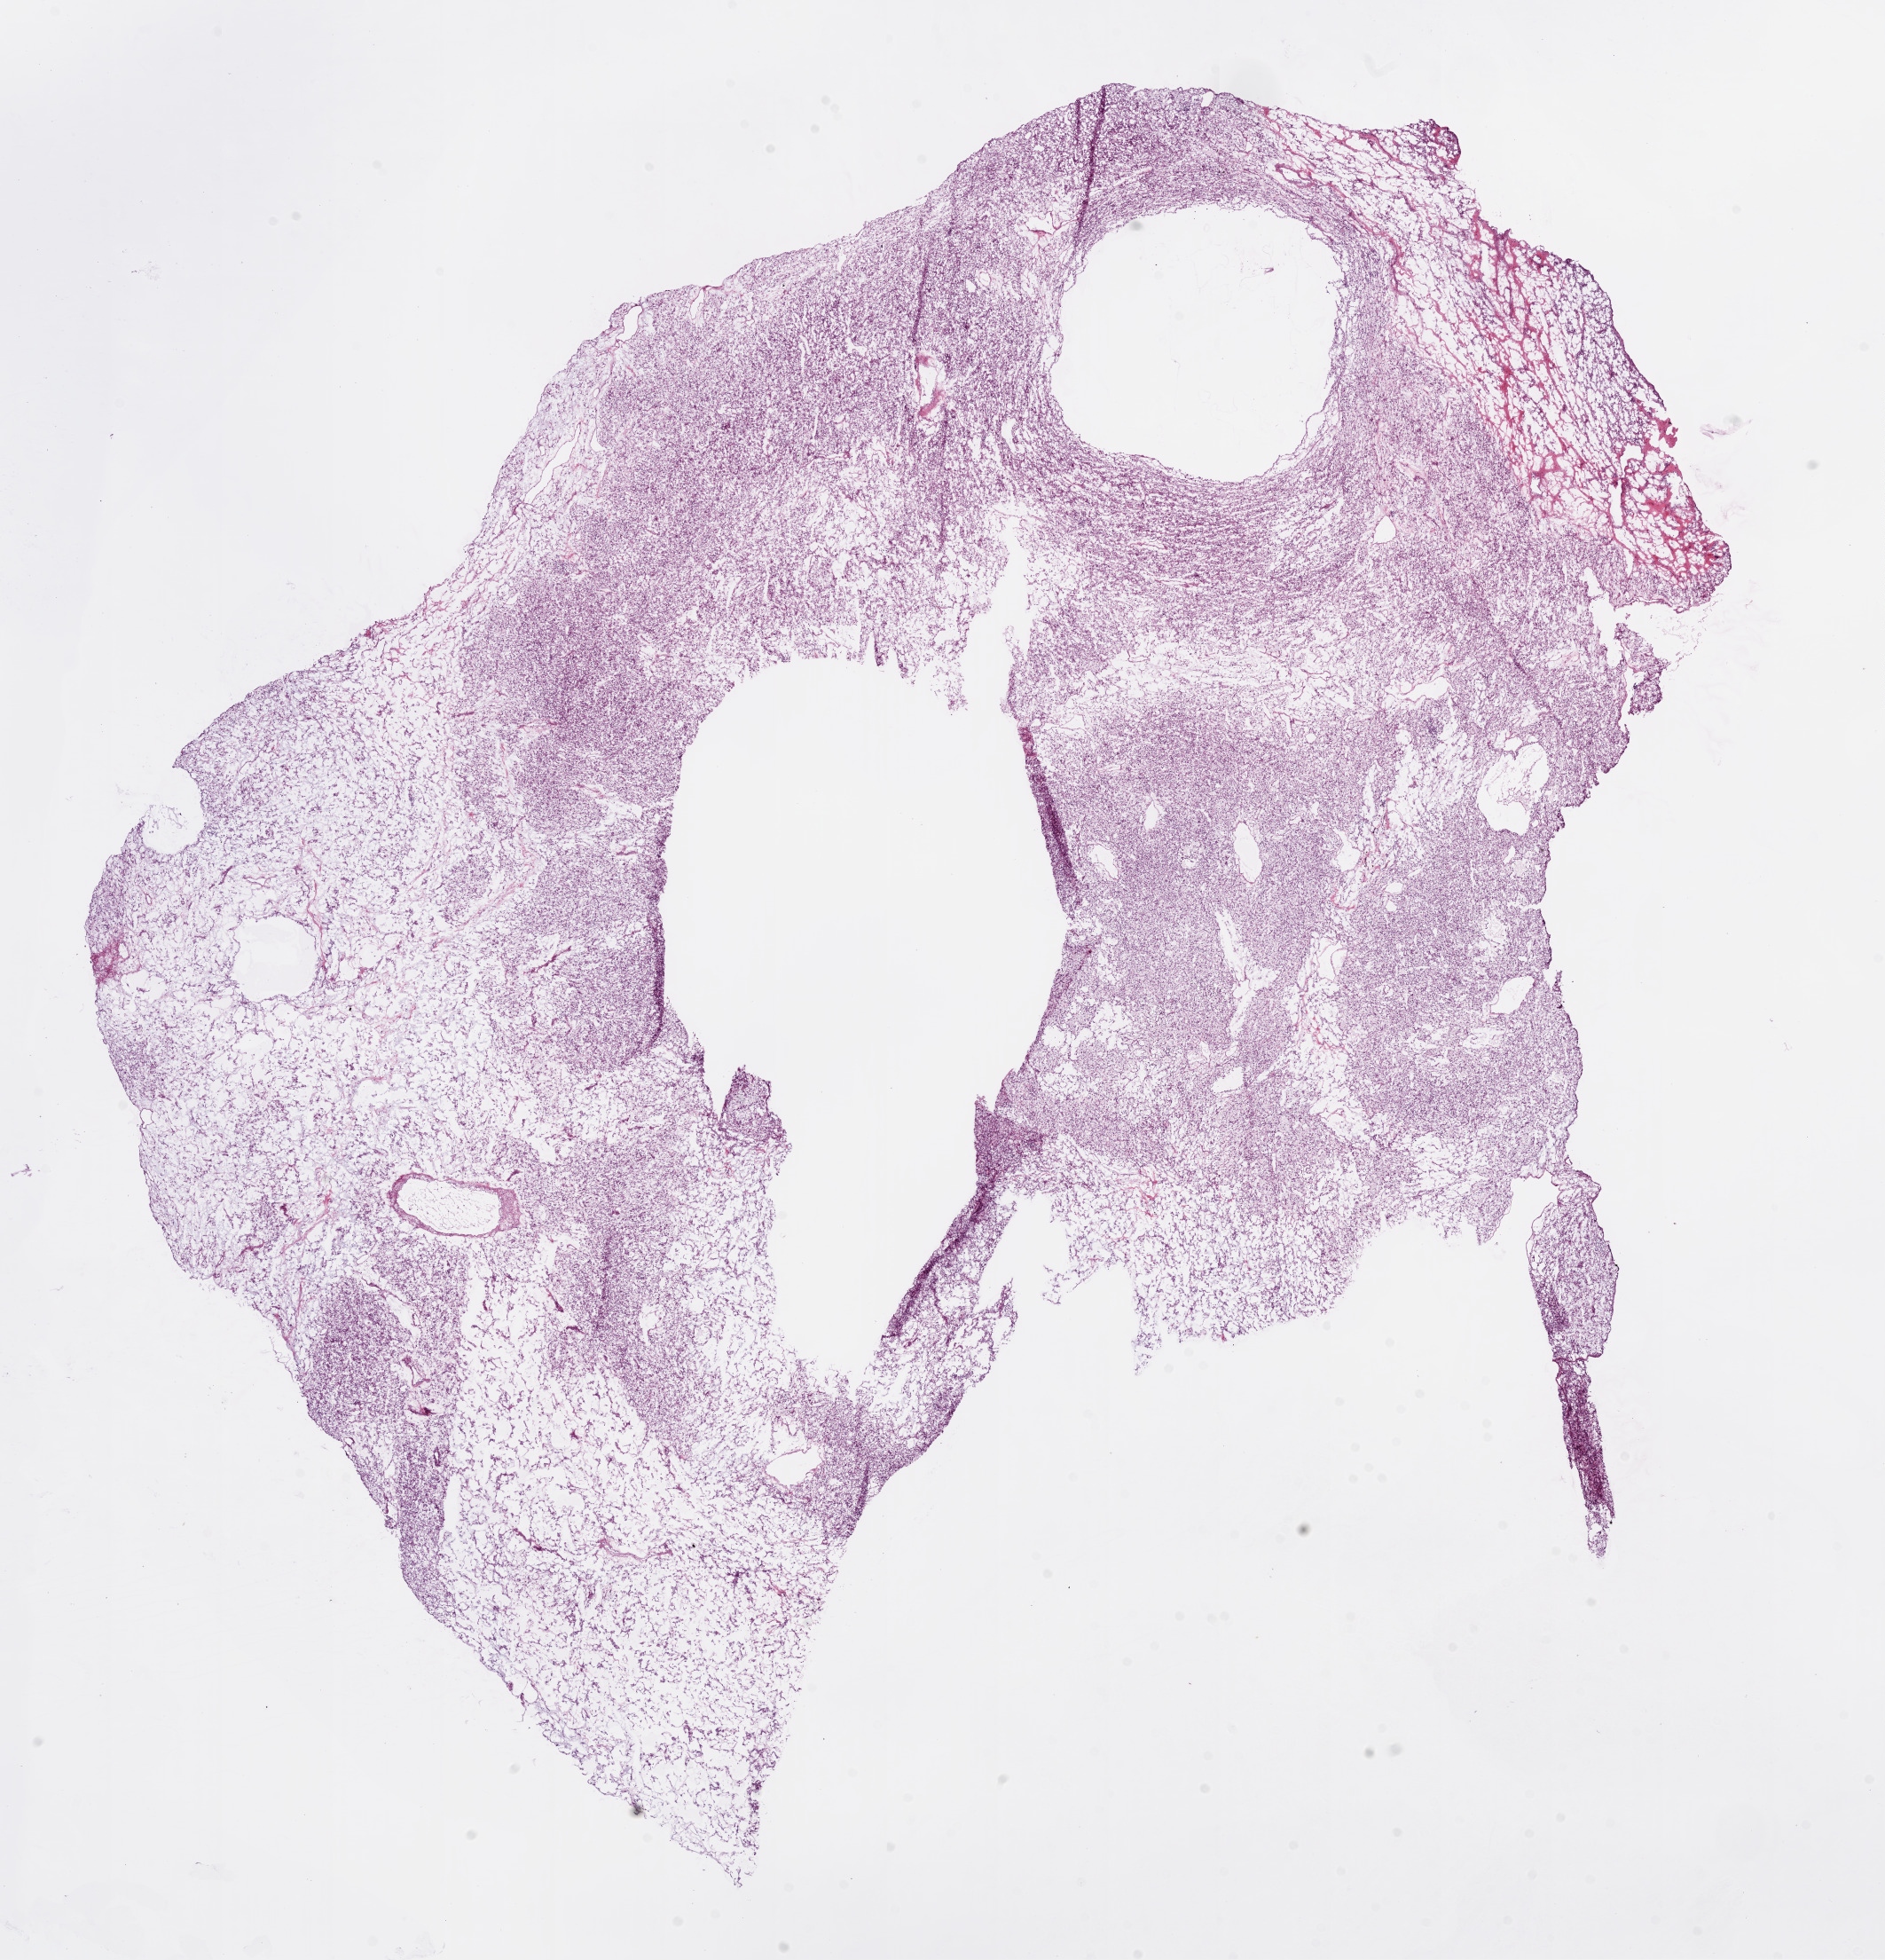
Whole-slide histology image, H&E-stained — low-resolution overview of the scanned area, about 17.1 x 17.7 mm (acquisition: 20x scan), frozen section from the bottom of the tissue portion, primary tumour sample from the kidney. Female patient; age at initial diagnosis 62 years. Histologic grade: G2 (moderately differentiated). Composition of this section per pathologist review: tumour cells 85%, tumour nuclei 85%, normal cells 0%, stromal cells 15%, necrosis 0%.
Pathologic diagnosis: Clear cell adenocarcinoma, NOS. Lymph nodes positive (case pathology): 0 of 4 examined. AJCC pathologic stage: I.